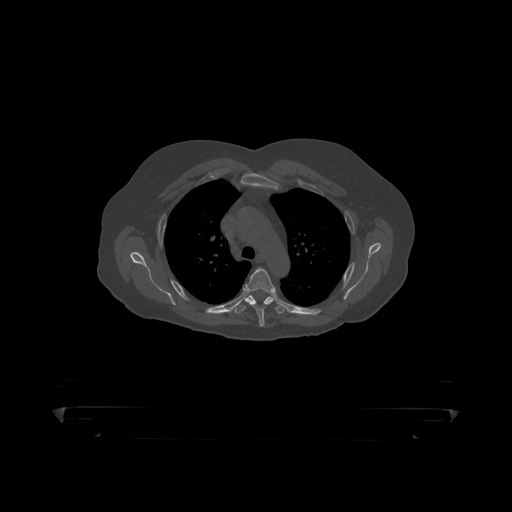
CT including the spine, one axial slice. Slice 332 of 390 in the series (ordered by position). Bone window (W 1800 / L 400 HU). 512 × 512 image matrix, field of view 650 × 650 mm. Male patient, age 60 years. Case-level facts recorded for this patient, not image findings: primary cancer: prostate.
Outlined on this slice (semi-automatically segmented with operator editing):
- T4 vertebra: bounding box <245,268,276,319> (left, top, right, bottom; pixels)
- T5 vertebra: <233,295,286,315>